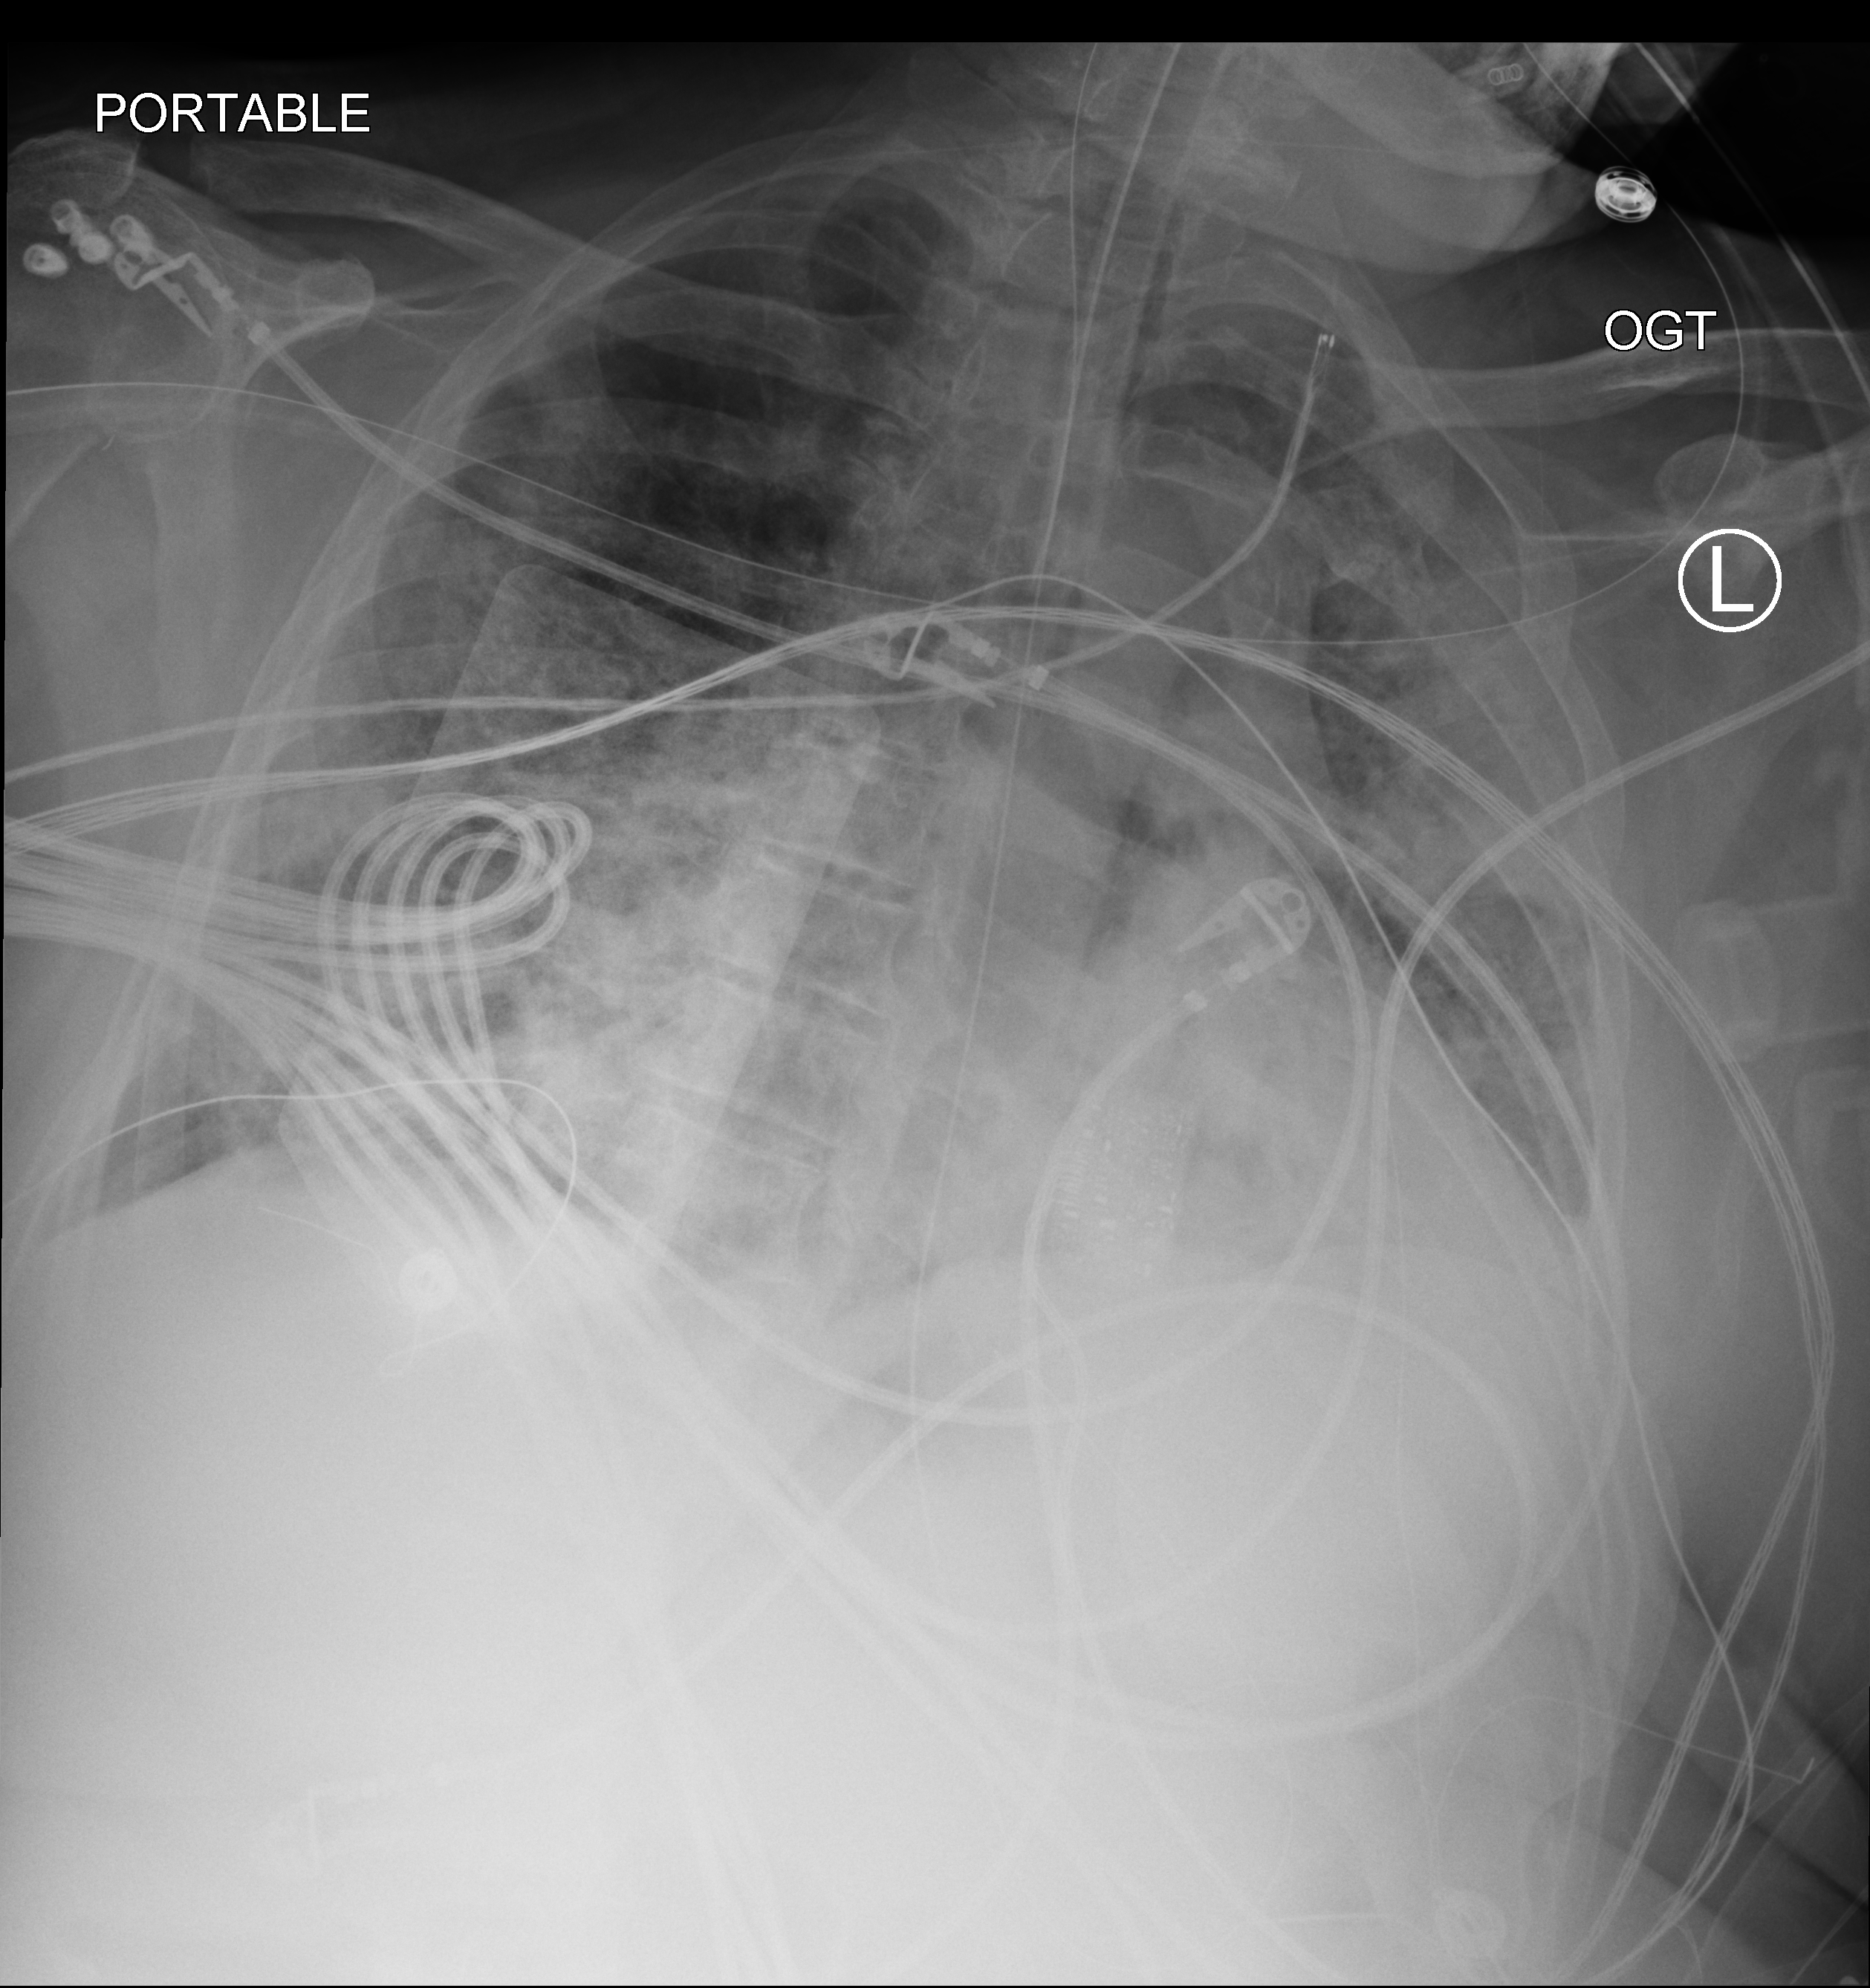
Portable chest radiograph. Female patient hospitalised with COVID-19, age 60–74 years.
From the hospital-stay record, not from the radiograph (when in the stay this image was taken is not recorded): length of hospital stay: 19 days; admitted to intensive care during this hospital stay: yes; mechanically ventilated during this hospital stay: yes.